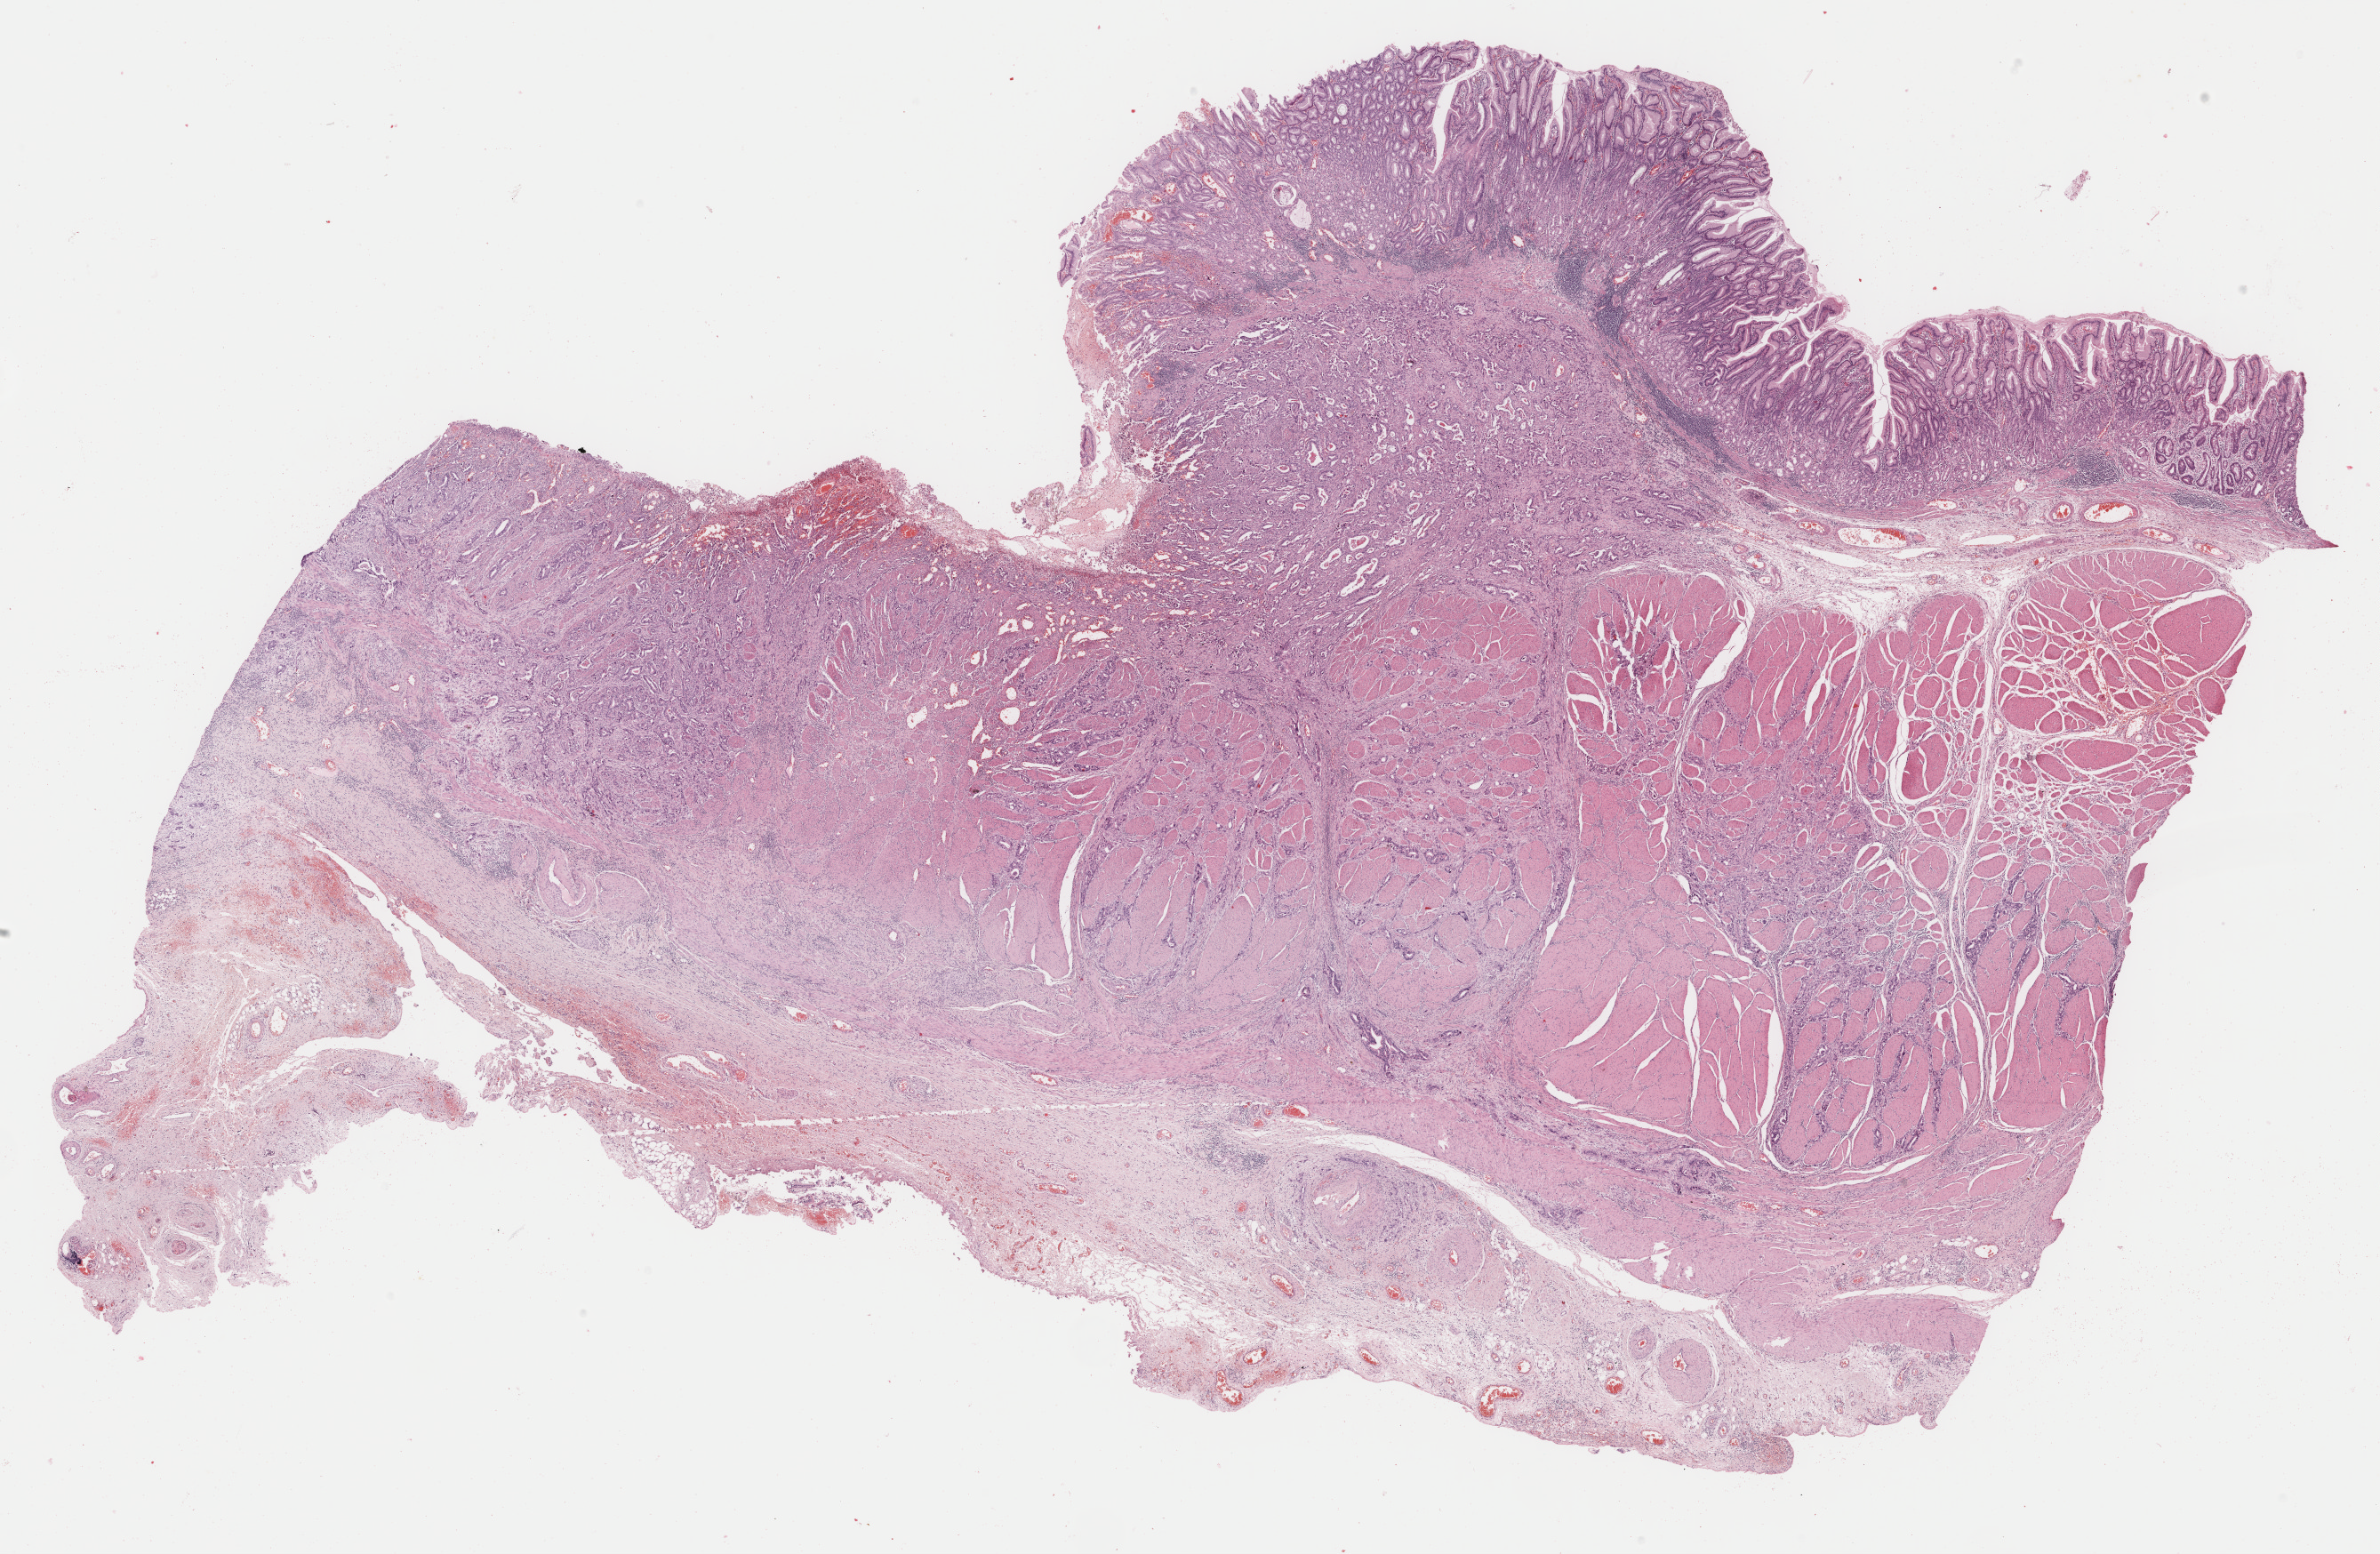
Whole-slide histology image, H&E — low-resolution overview of the scanned area, about 21.2 x 13.9 mm; formalin-fixed paraffin-embedded (FFPE) diagnostic section; primary tumour sample from the stomach. Male, age 72 years at initial diagnosis.
Pathologic diagnosis: Adenocarcinoma, NOS.